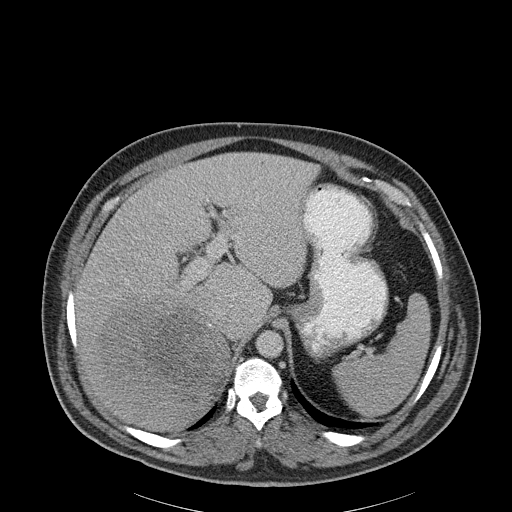
Contrast-enhanced abdominal CT, one axial slice. Position 147 of 186 along the scan axis. Reconstruction kernel B30f. 120 kVp. Soft-tissue window (W 400 / L 40 HU). 512 × 512 image matrix, field of view 464 × 464 mm. Patient: male, 56 years. From the clinical record (not read from this slice): diagnosis: adrenocortical carcinoma; tumour side: right adrenal; tumour size at pathology: 18 cm.
Annotated regions visible in this slice (semi-automatically segmented with operator editing):
- mass: bounding box [x1, y1, x2, y2] px = [102, 299, 226, 397]